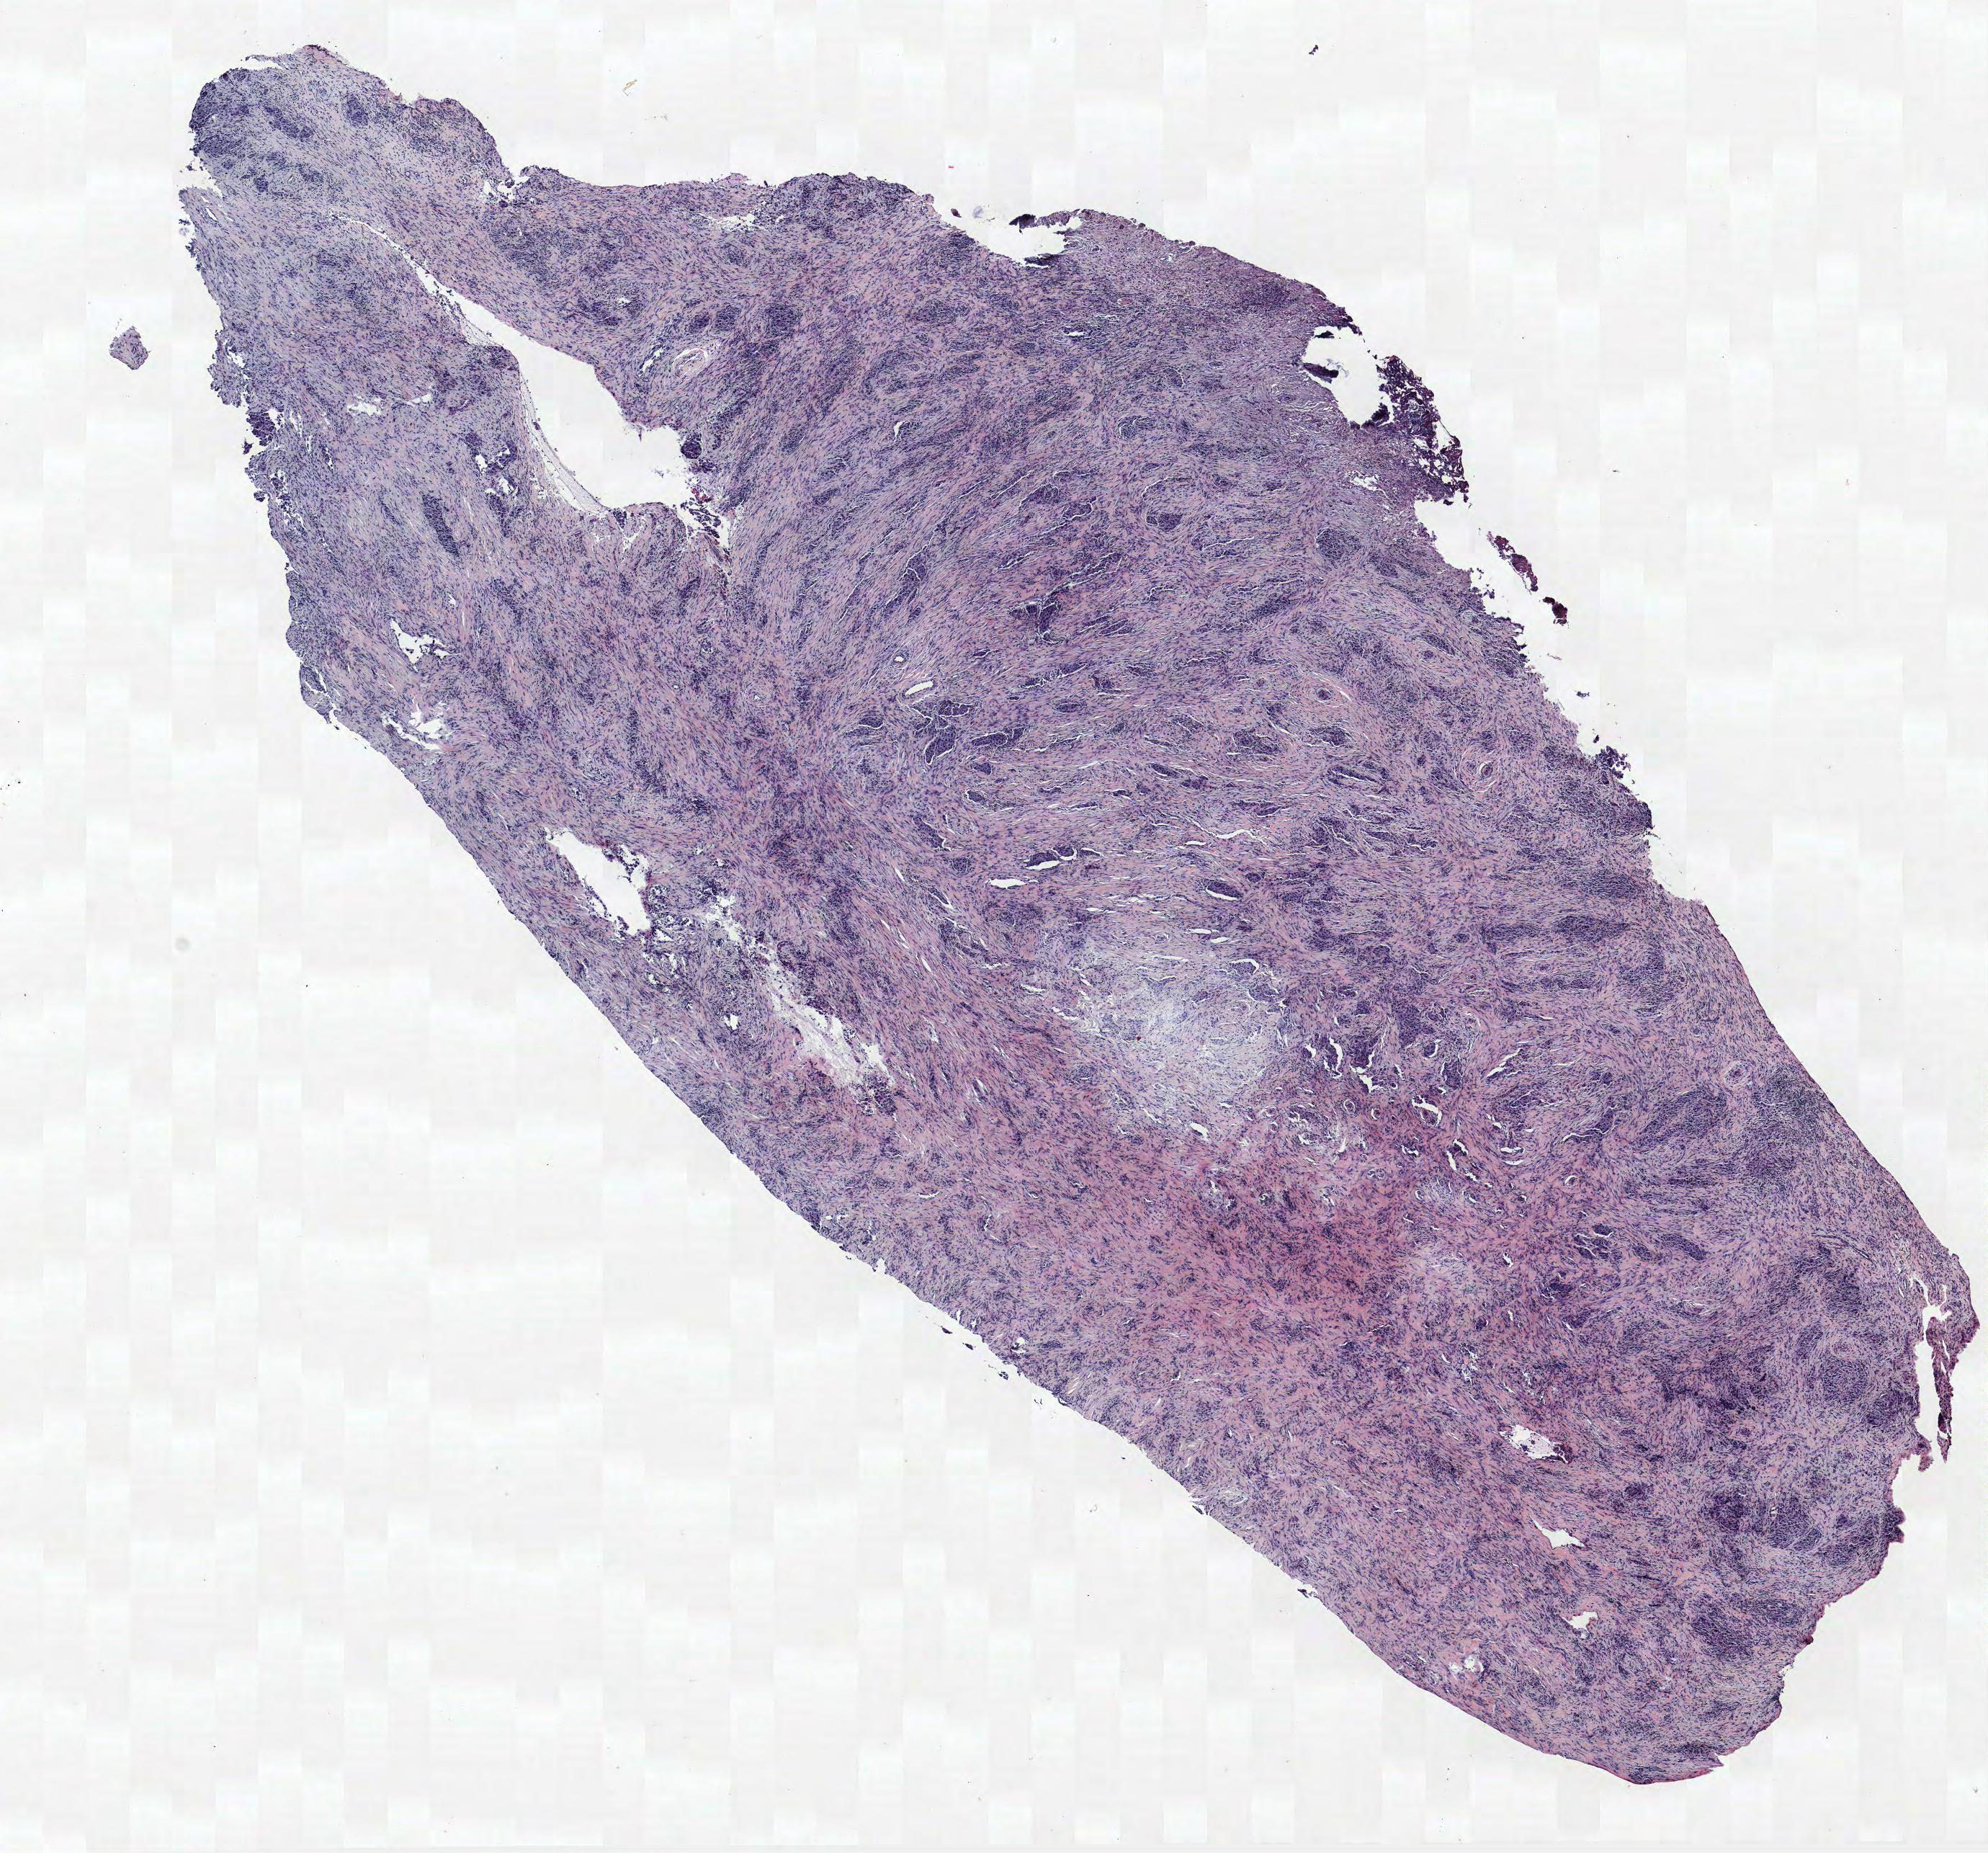
Whole-slide histology image, Hematoxylin and eosin (H&E) stained — whole scanned area (about 11.0 x 10.3 mm) shown as a low-resolution overview. Formalin-fixed paraffin-embedded (FFPE) section. Lung tissue. Female patient, aged 70 at enrolment. Former smoker at enrolment.
Participant's lung-cancer diagnosis: Non-small cell carcinoma.